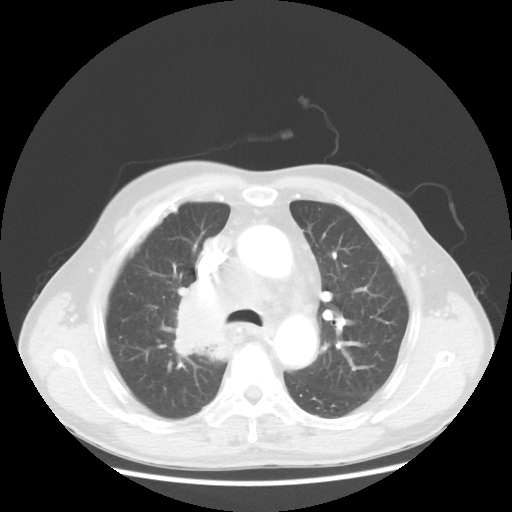
Chest CT, one axial slice. Position 83 of 124 along the scan axis. 100 kVp. Lung window (W 1500 / L -600 HU). 5 mm slice thickness. 512 × 512 image matrix, field of view 382 × 382 mm. Patient: male, 64 years. Case-level facts recorded for this patient, not image findings: clinical TNM (as recorded): T3 N3 M0.
Outlined on this slice (bounding box drawn by a radiologist):
- lung tumour (recorded histology: small cell carcinoma): box from (x=169, y=284) to (x=251, y=363) px